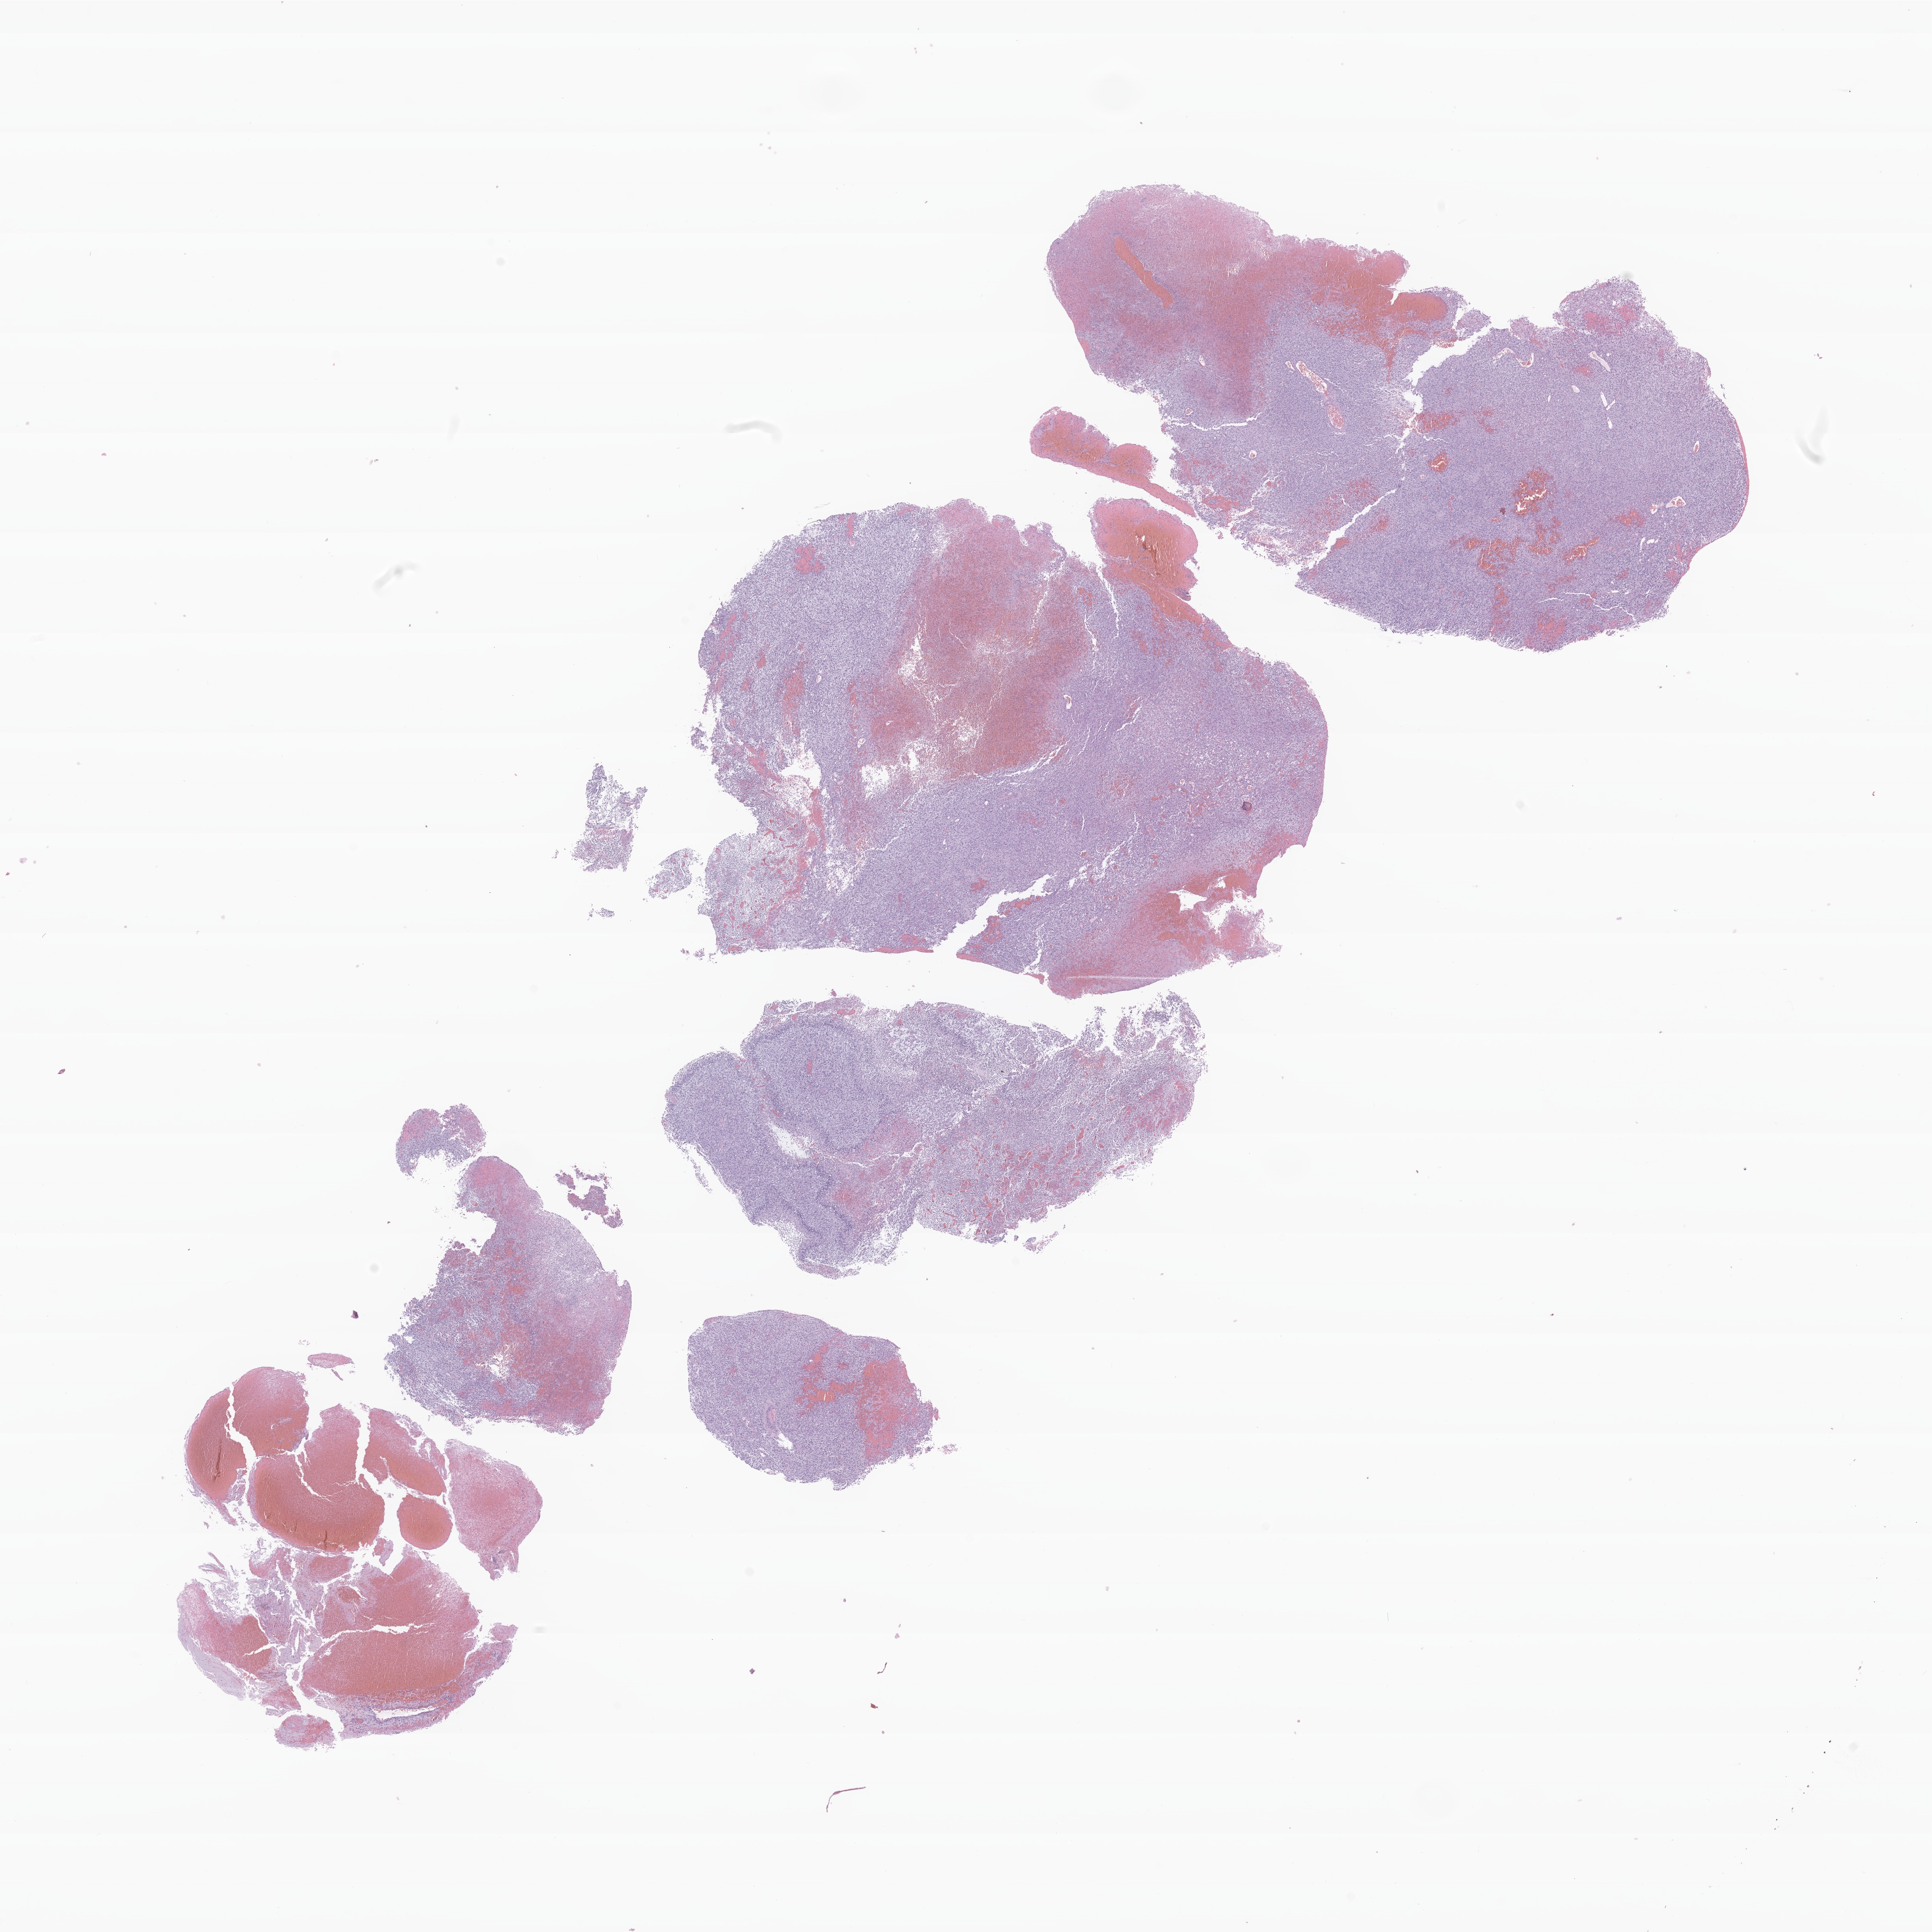
Digitized H&E-stained section of tumor tissue from the brain — shown as a low-resolution overview of the whole scanned area (about 20.6 x 20.6 mm); FFPE section. Patient: male, age 48 months (4 years).
Diagnosis (ICD-O-3 morphology term): Glioma, malignant.